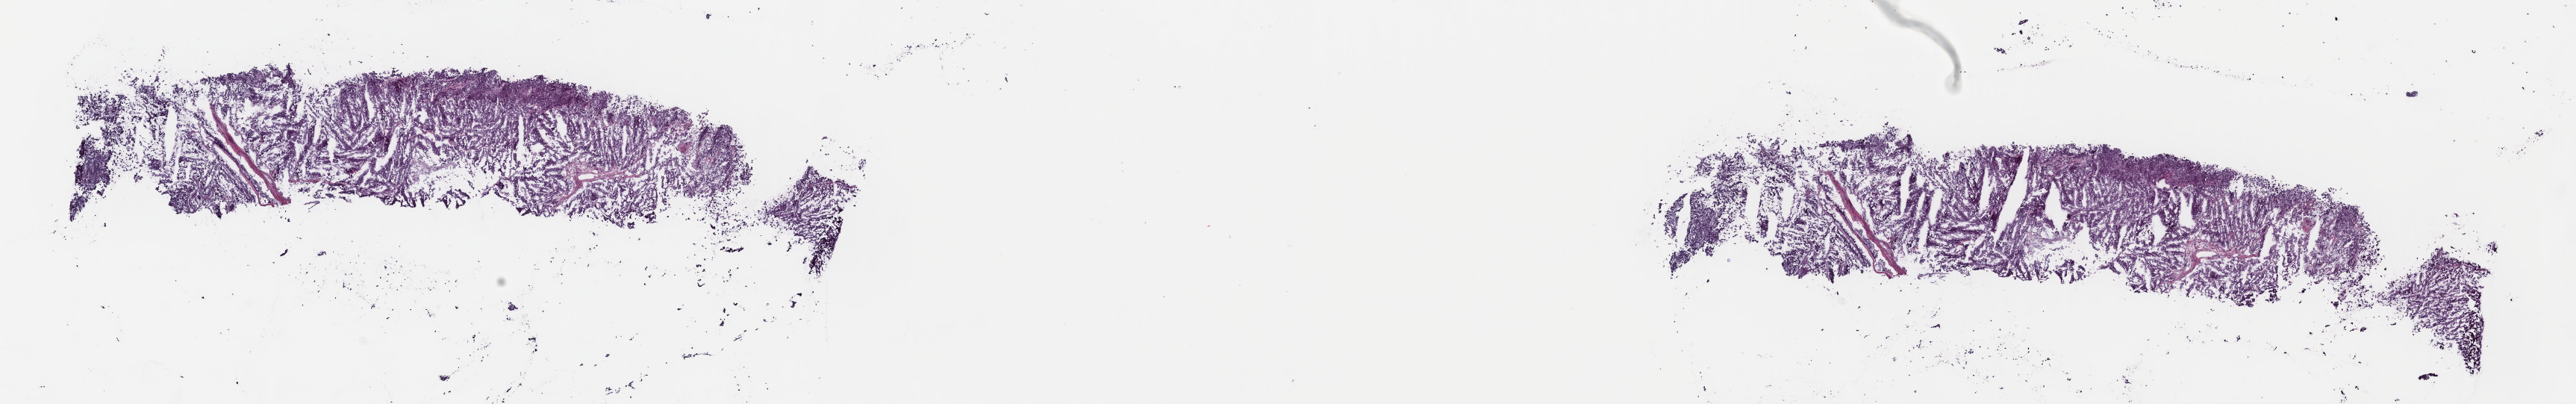
Whole-slide histology image, H&E-stained — a low-resolution overview of the entire scanned area, about 27.1 x 4.3 mm (slide scanned at 40x); frozen section from the top of the tissue portion; primary tumour sample from the adrenal cortex. Patient: female, age at initial diagnosis 61 years. Composition of this section per pathologist review: tumour cells 100%, tumour nuclei 95%, normal cells 0%, stromal cells 0%, necrosis 0%. Inflammatory infiltration, as recorded: lymphocyte infiltration 0%, monocyte infiltration 0%, neutrophil infiltration 0%.
• diagnosis: Adrenal cortical carcinoma (cortex of adrenal gland)
• laterality: right